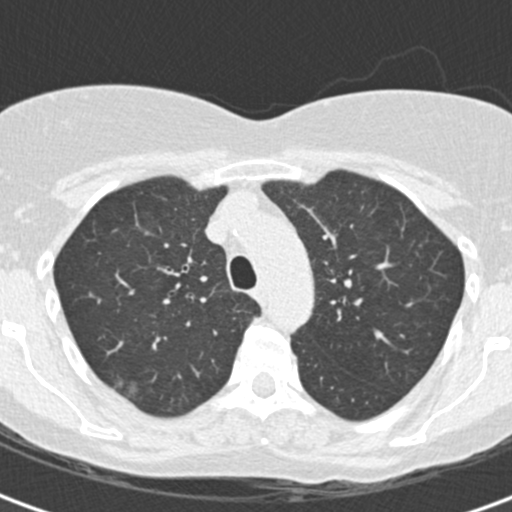
Low-dose screening chest CT, one axial slice. Position 130 of 172 along the scan axis. Reconstruction kernel B30f. 120 kVp. Lung window (W 1500 / L -600 HU). 2 mm slice thickness. 512 × 512 image matrix.
Structures marked on this image (expert manual segmentation):
- lesion 1 (tumor, upper lobe of right lung): box from (x=114, y=377) to (x=140, y=397) px